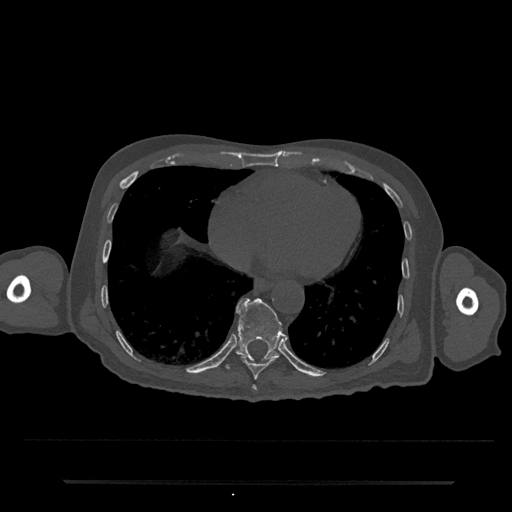
CT including the spine, one axial slice. Slice 340 of 797 in the series (ordered by position). 120 kVp. Bone window (W 1800 / L 400 HU). 0.5 mm slice thickness. 512 × 512 image matrix. Patient: male, 74 years. Case-level facts recorded for this patient, not image findings: primary cancer: prostate.
Annotated regions visible in this slice (semi-automatically segmented with operator editing):
- T10 vertebra: bounding box [x1, y1, x2, y2] px = [226, 298, 285, 369]
- T8 vertebra: [252, 385, 257, 391]
- T9 vertebra: [240, 355, 277, 380]